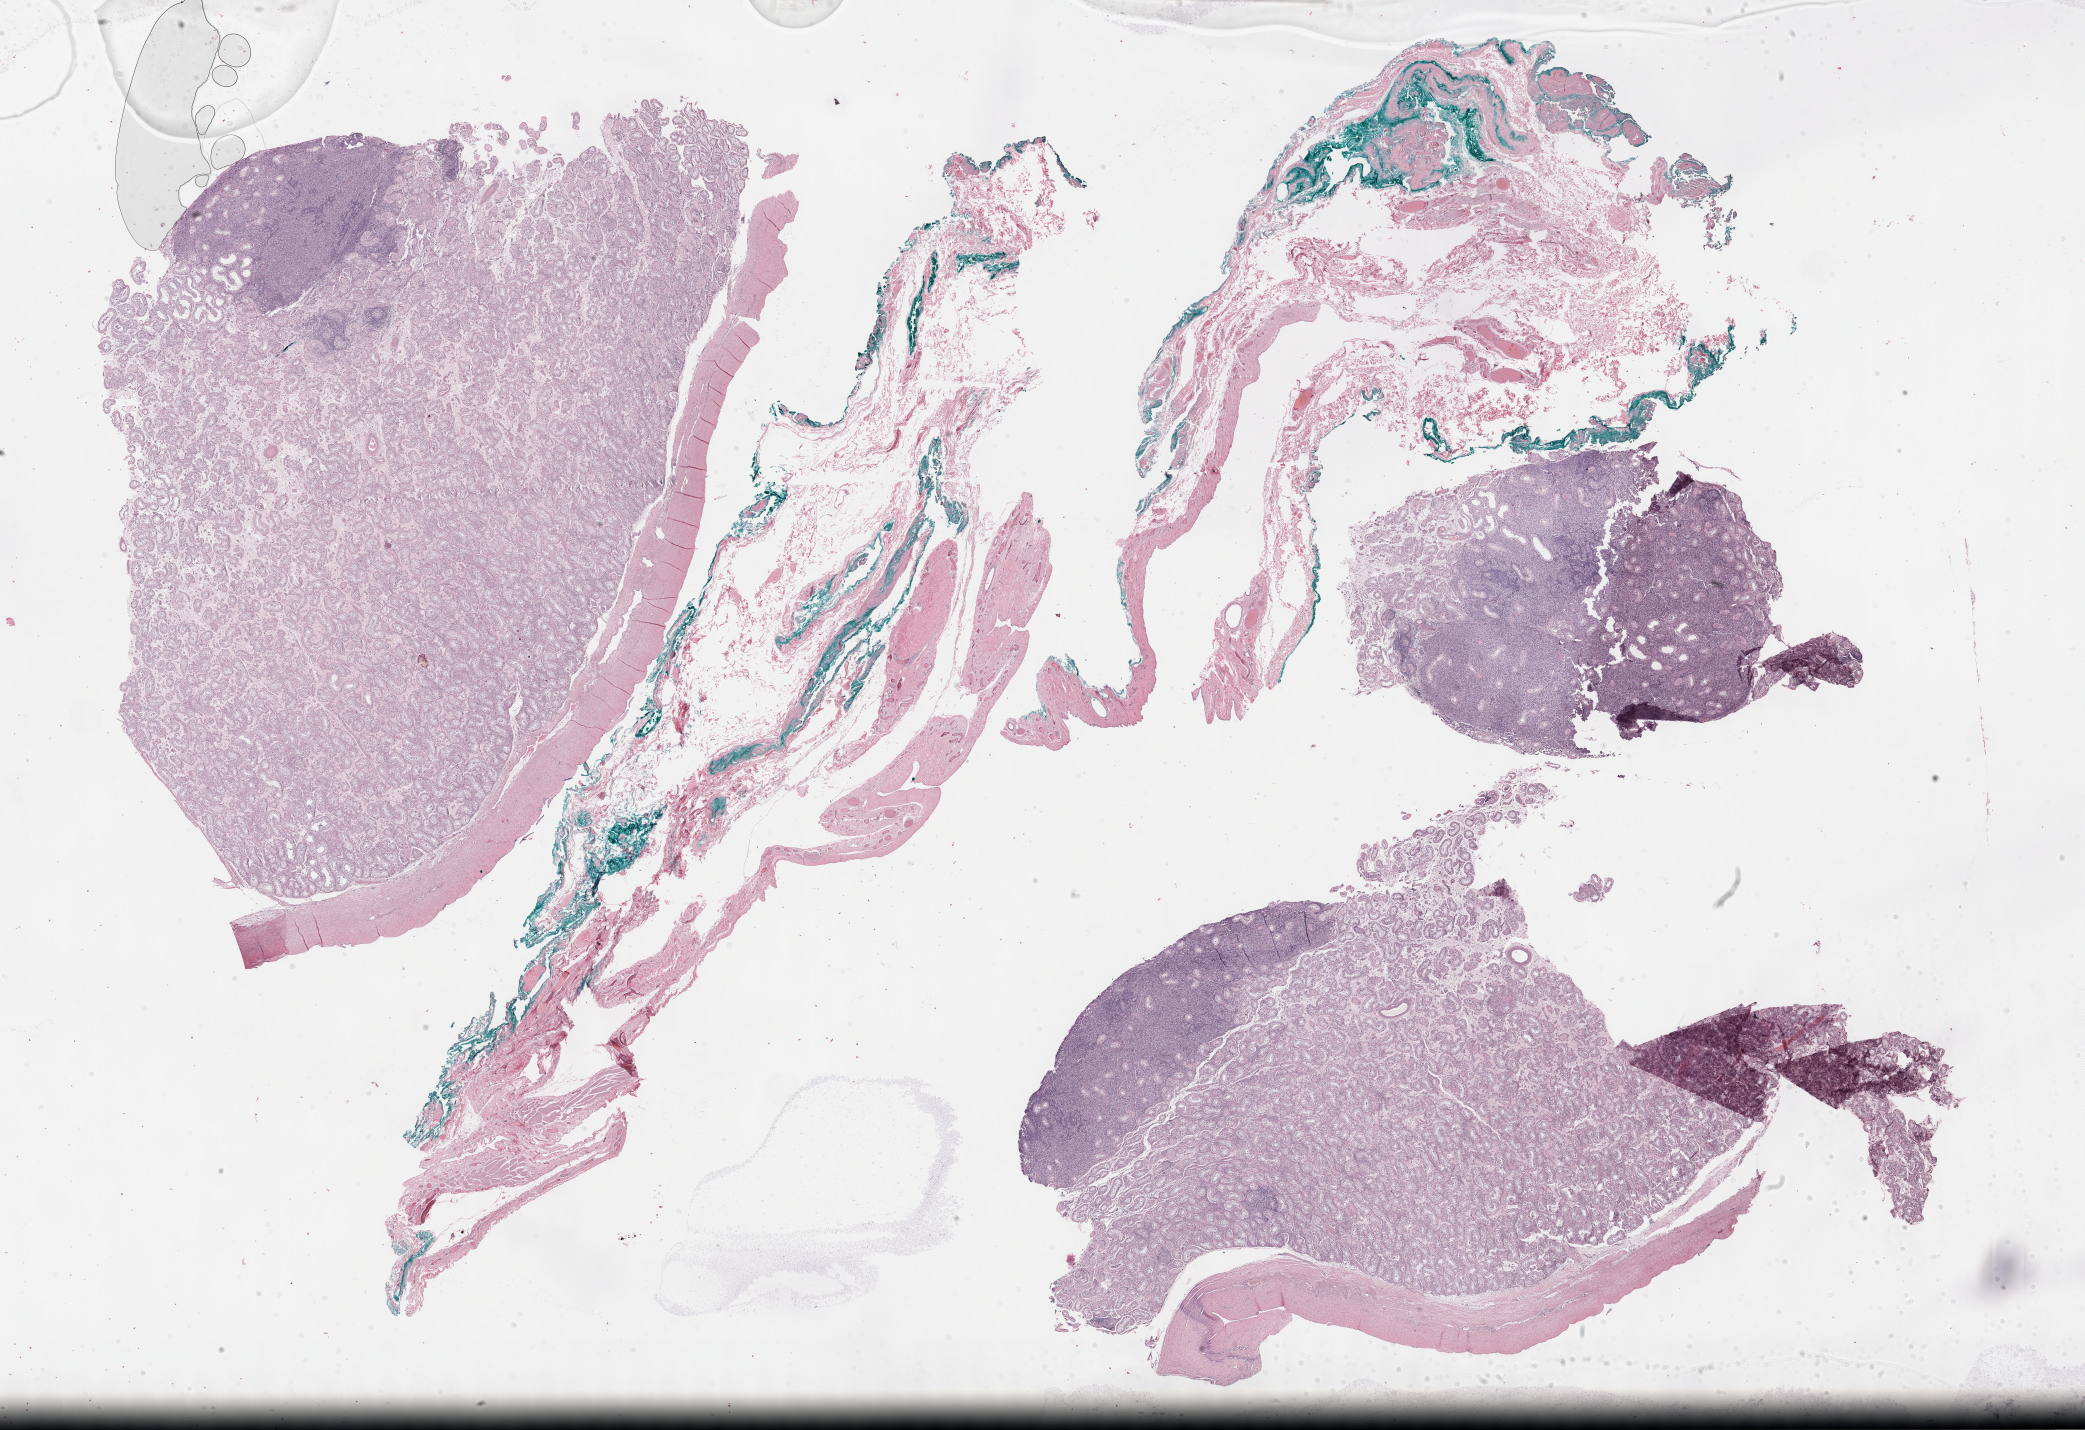
Digitized H&E tissue section (whole slide), a low-resolution overview of the entire scanned area, about 33.7 x 23.1 mm, FFPE section, testis, primary tumour sample. Male patient; age at initial diagnosis 29 years.
Pathologic diagnosis: Seminoma, NOS.